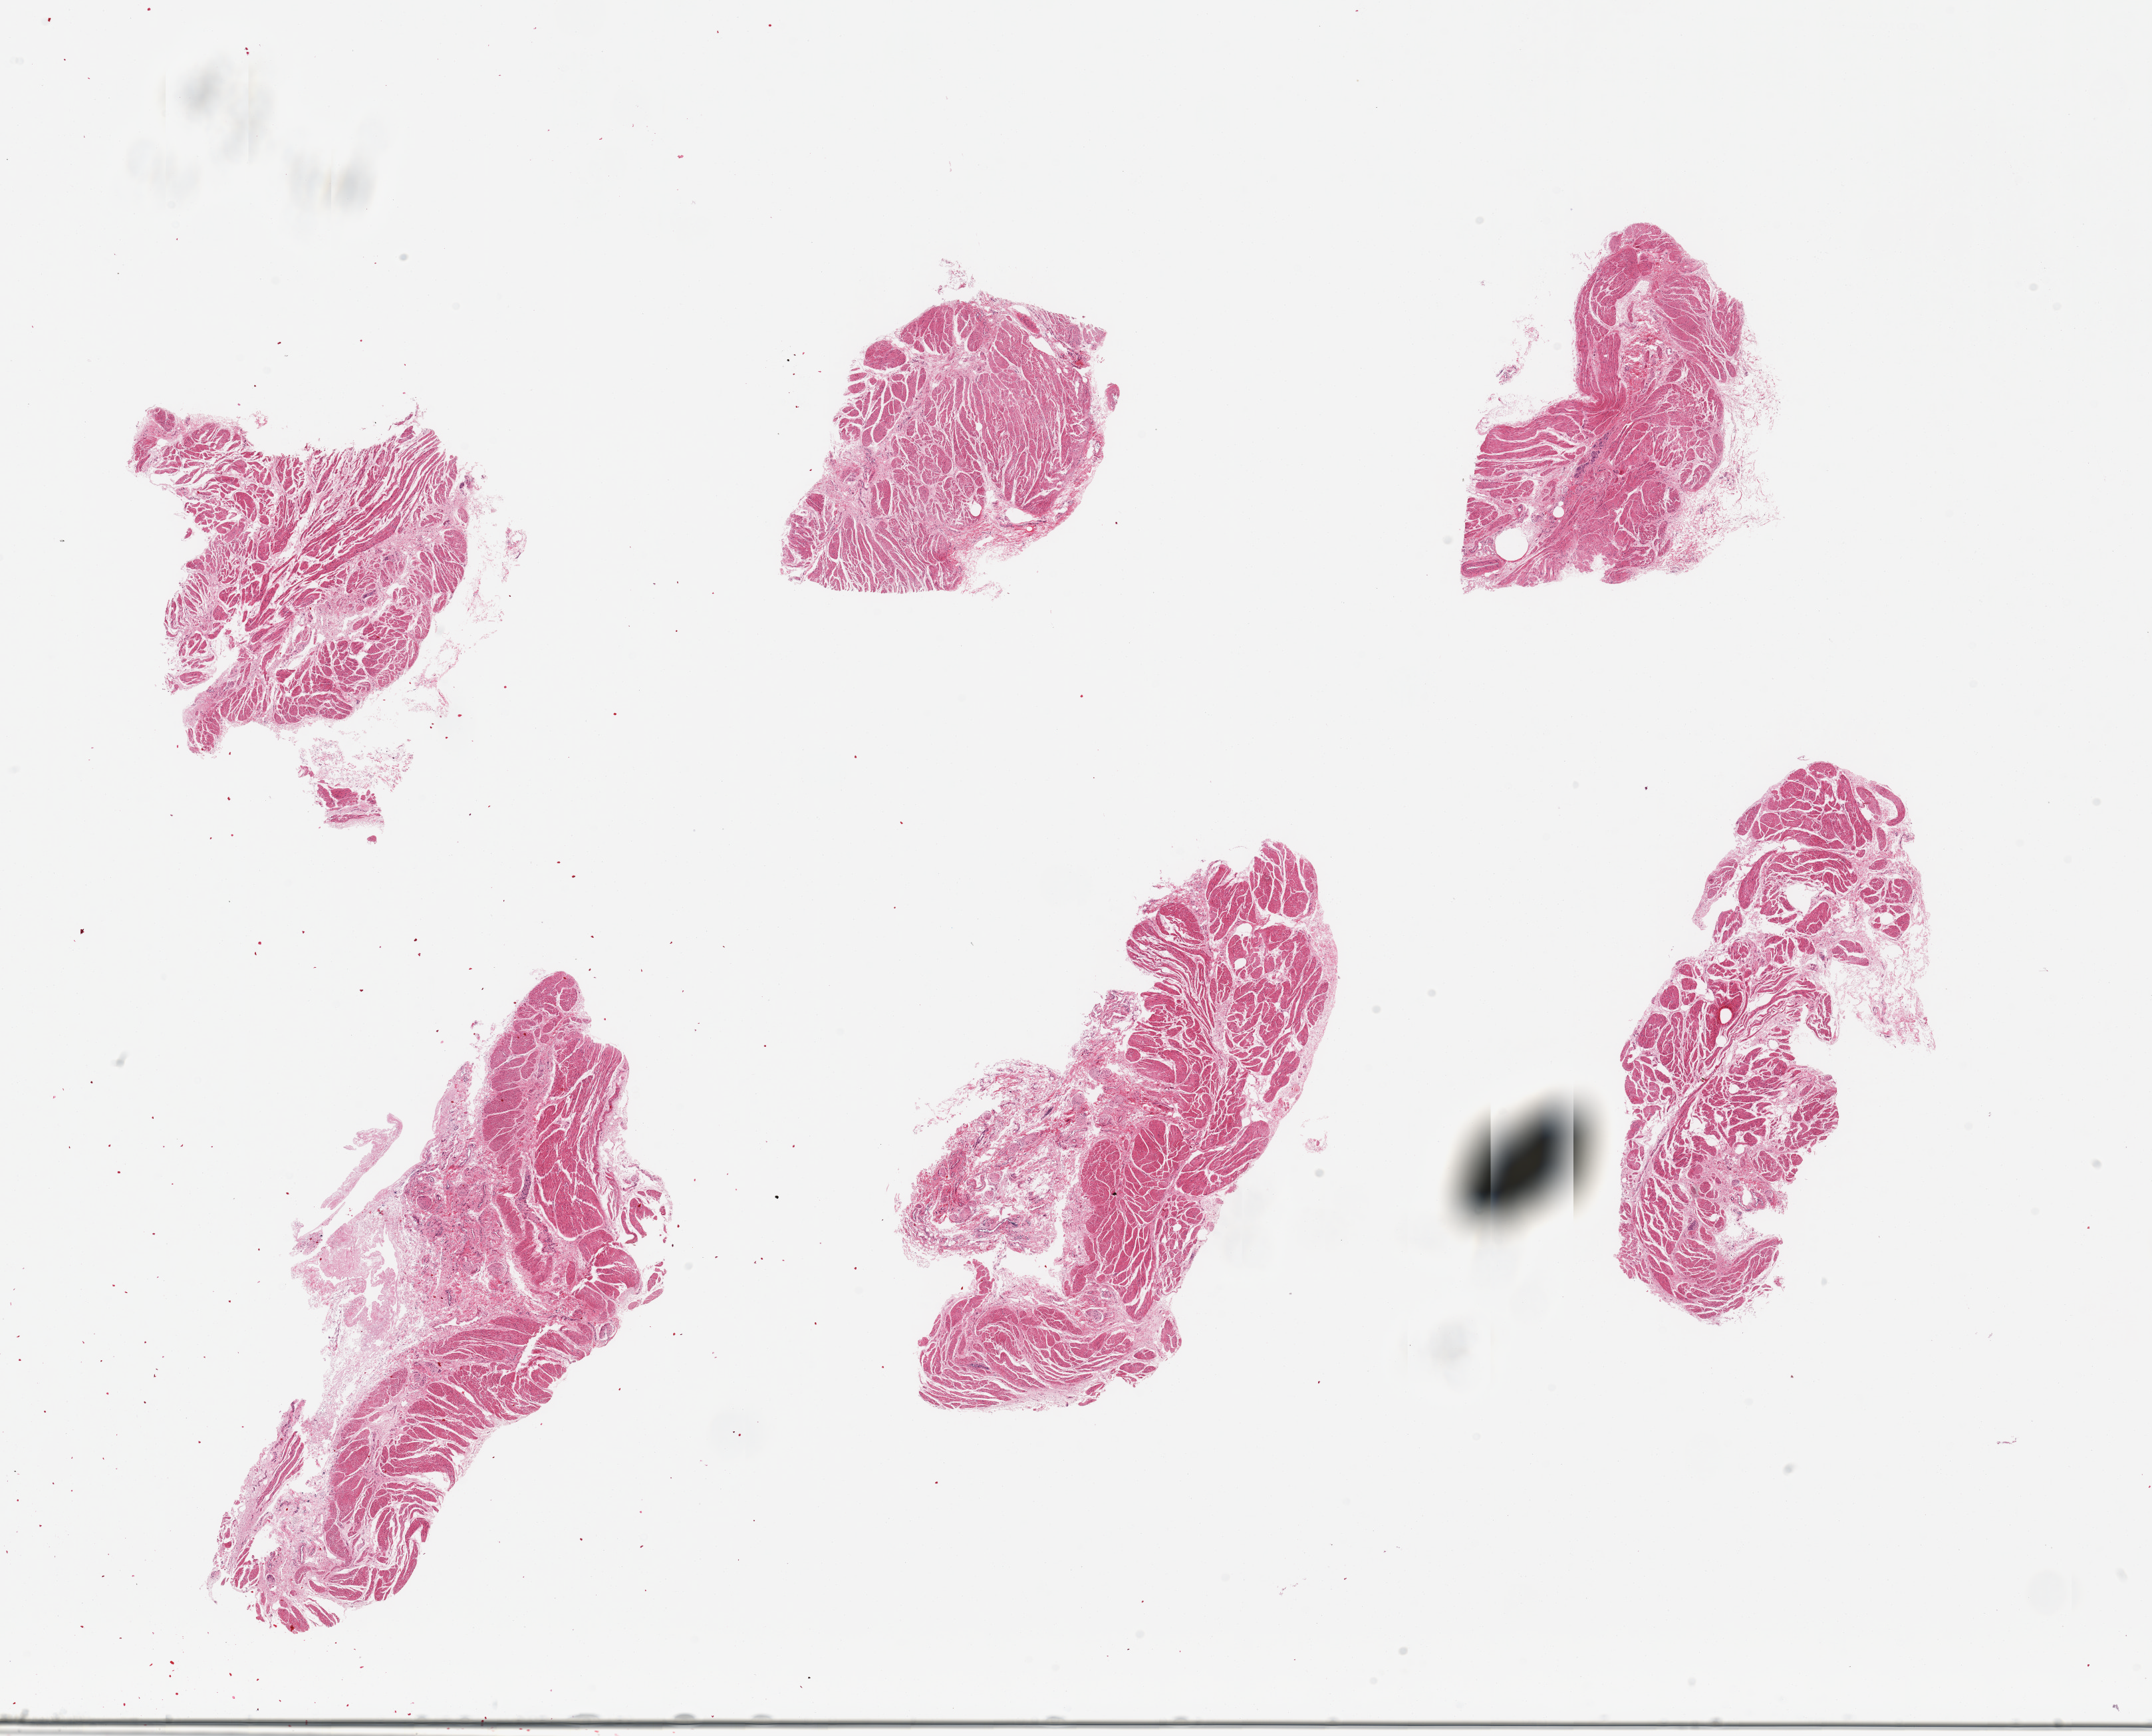
Digitized haematoxylin and eosin-stained section, shown as a low-resolution overview of the whole scanned area (about 25.6 x 20.6 mm). PAXgene-fixed paraffin-embedded (PFPE) section. Target tissue: gastroesophageal junction. Donor tissue sample.
- pathologist's review note for this sample: 6 pieces: 2 have abundant submucosal stroma